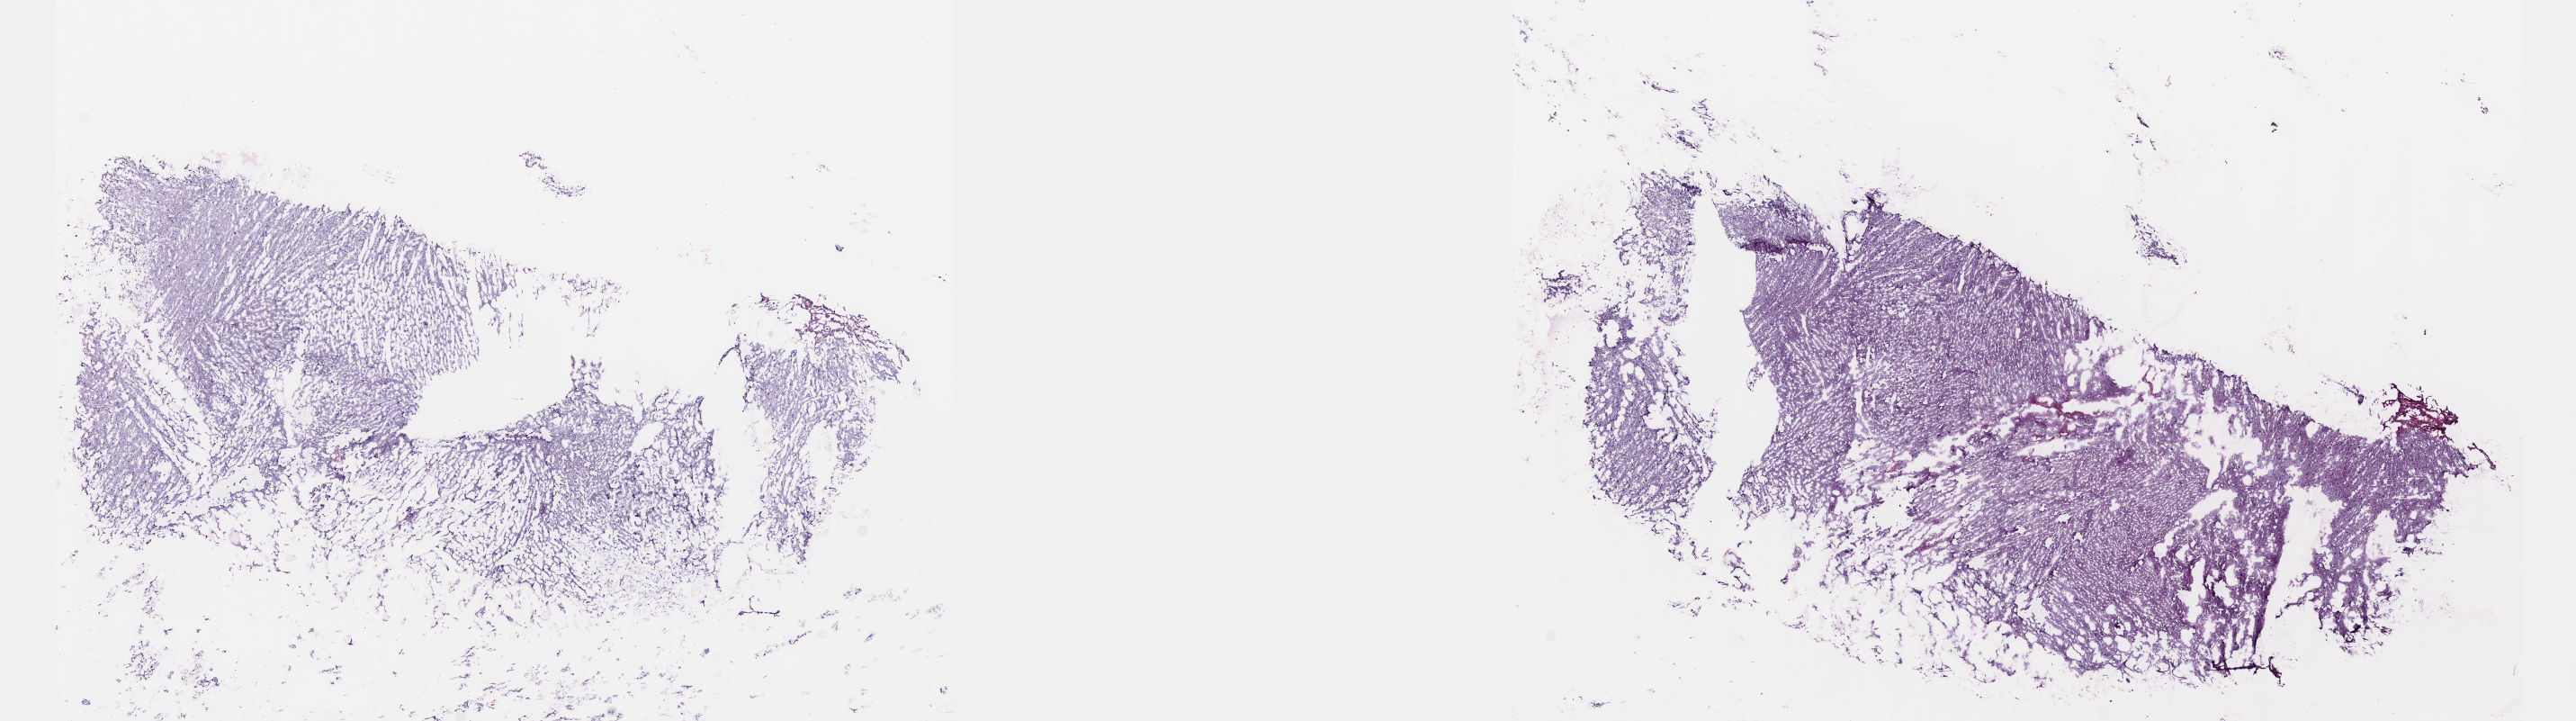
Digitized Hematoxylin and eosin (H&E) stained tissue section (whole slide) — whole scanned area (about 23.1 x 6.5 mm, from a 40x scan) shown as a low-resolution overview. Frozen section from the top of the tissue portion. Primary tumour sample from the brain. Female, age 41 years at initial diagnosis. Histologic grade: G2 (moderately differentiated). Slide review estimates, as recorded: tumour cells 30%, tumour nuclei 70%, normal cells 10%, stromal cells 60%, necrosis 0%. Inflammatory infiltration, as recorded: lymphocyte infiltration 0%, monocyte infiltration 0%, neutrophil infiltration 0%.
Laterality: right. Pathologic diagnosis: Astrocytoma, NOS (cerebrum).